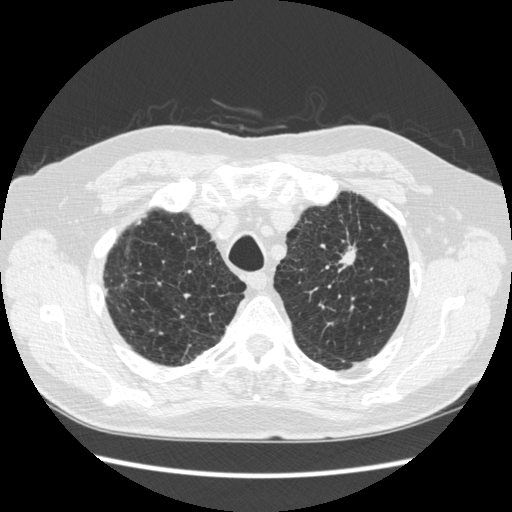
Low-dose screening chest CT, one axial slice; slice 222 of 267 in the series (ordered by position); reconstruction kernel STANDARD; 120 kVp; lung window (W 1500 / L -600 HU); 1.25 mm slice thickness; 512 × 512 image matrix, field of view 360 × 360 mm.
Structures marked on this image (outlined manually by an expert reader):
- lesion 1 (tumor, upper lobe of left lung): bounding box [x1, y1, x2, y2] px = [339, 240, 356, 267]